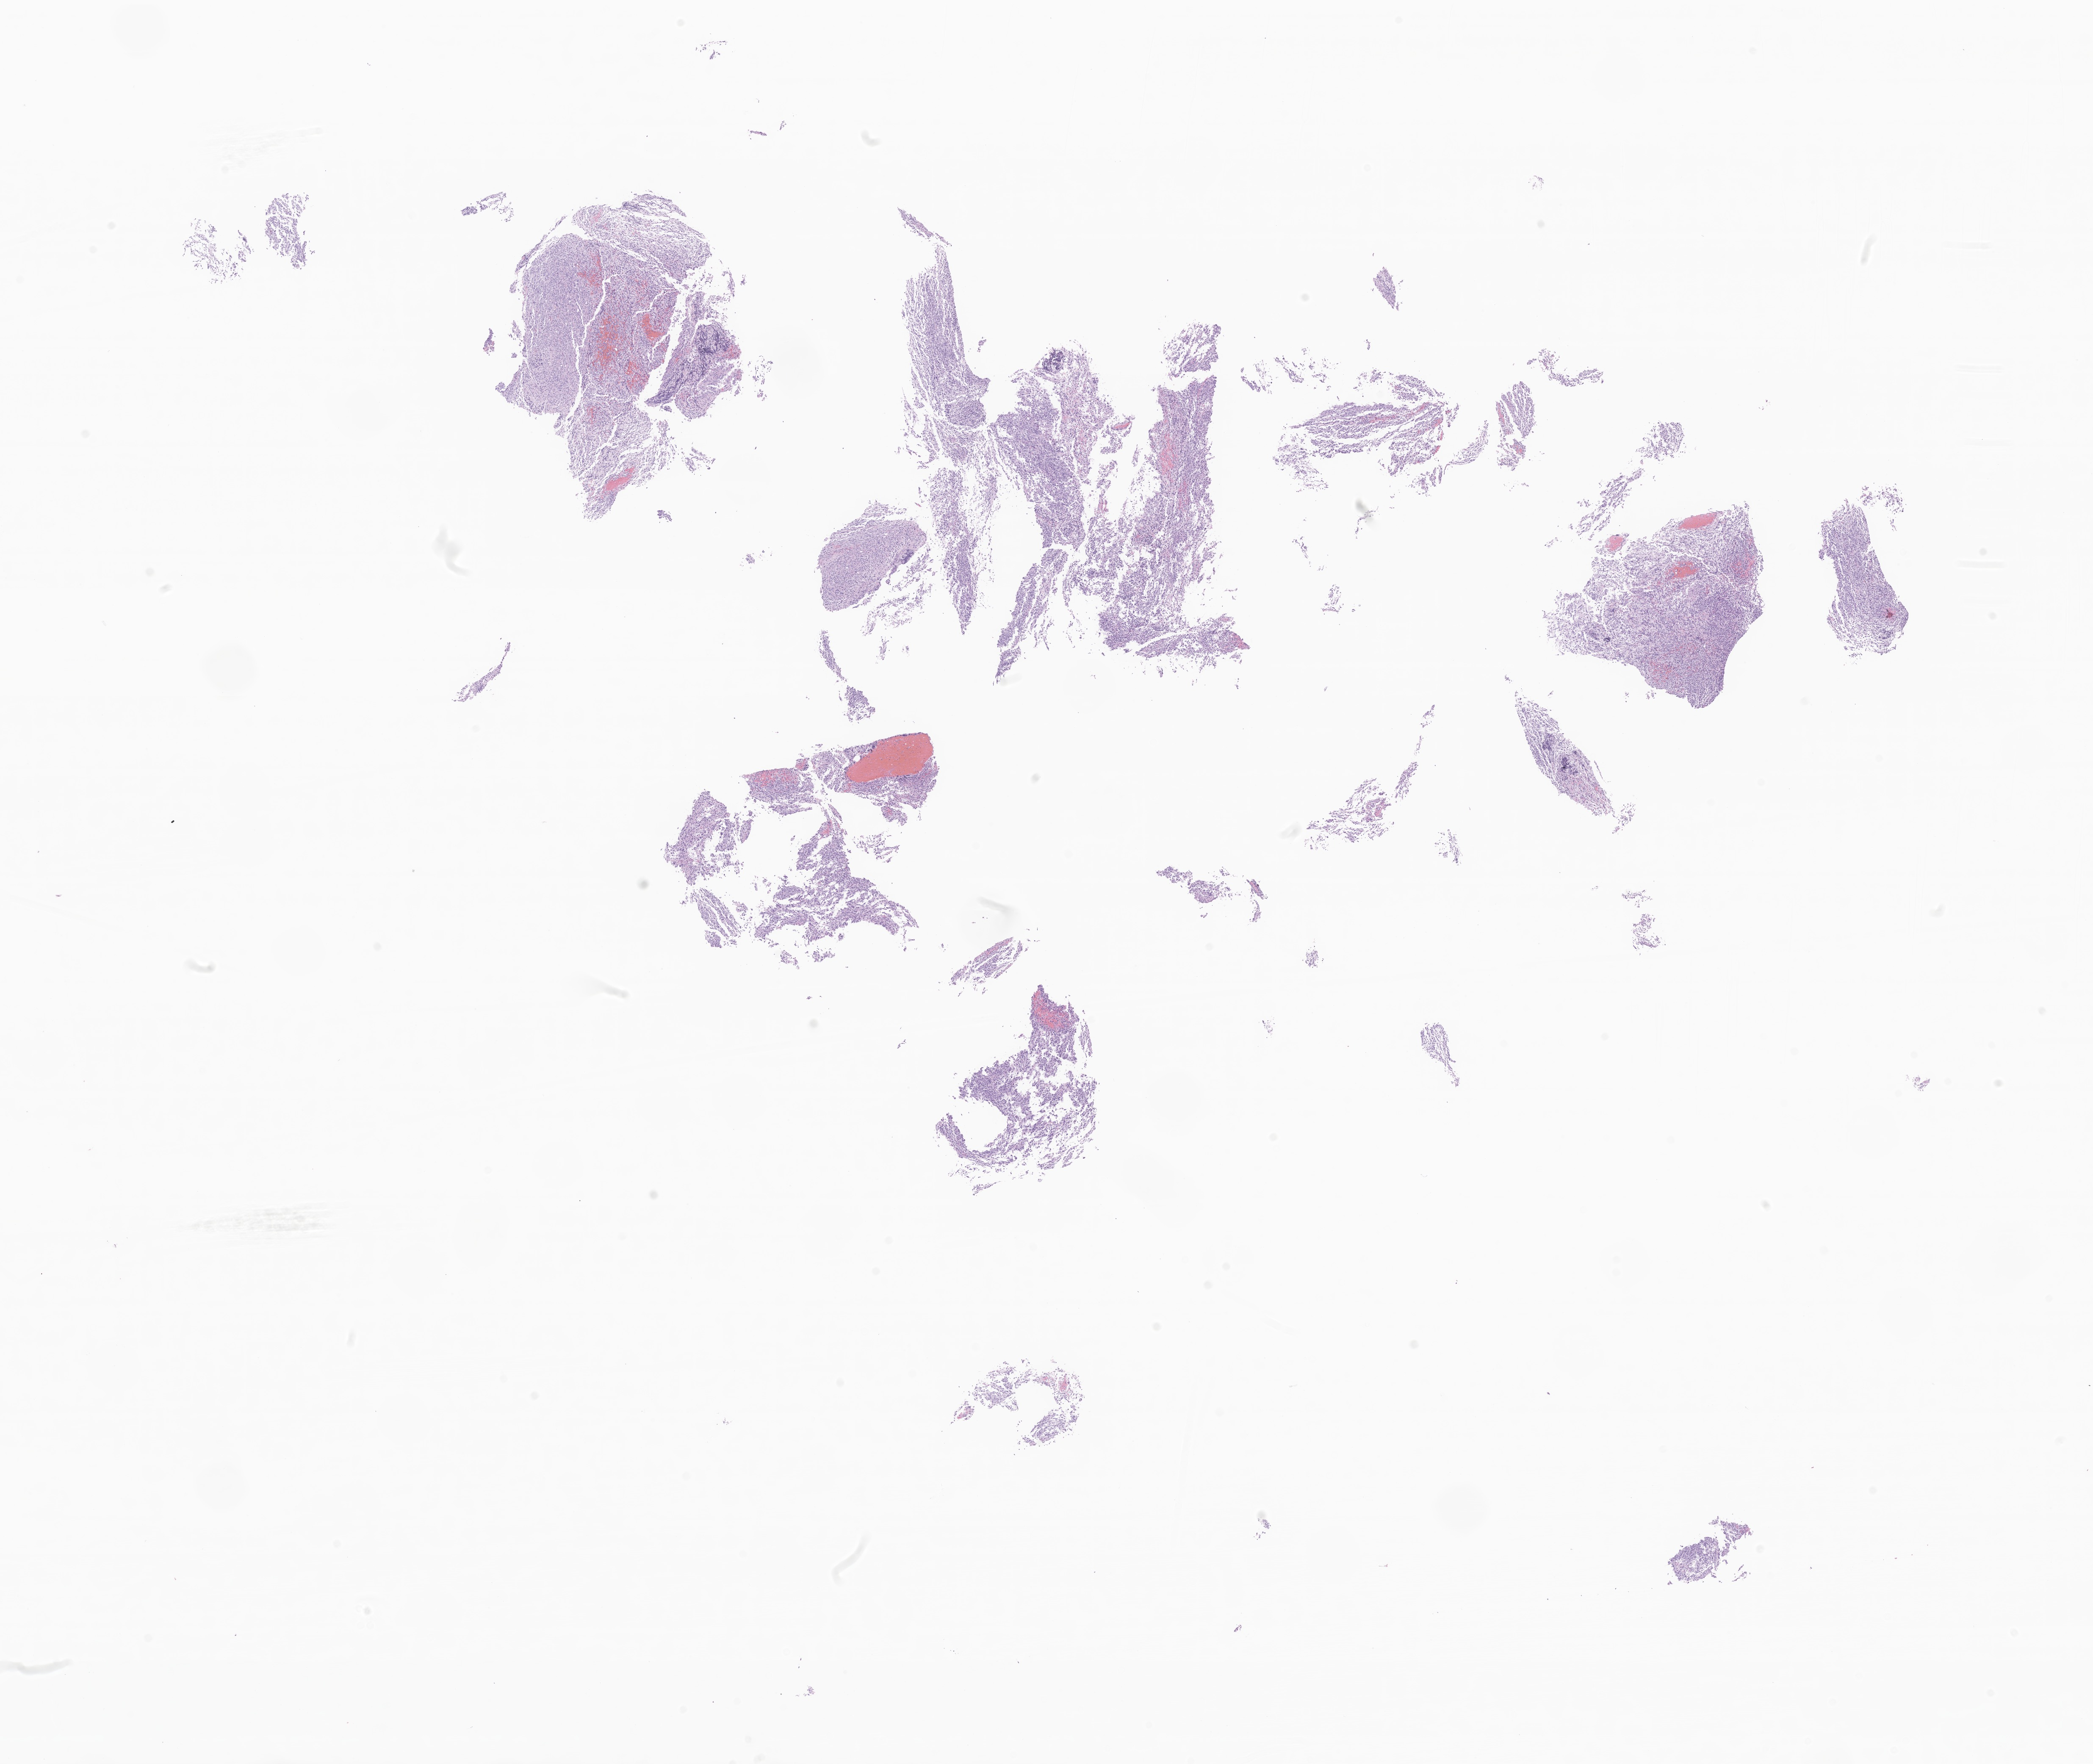
Digitized hematoxylin and eosin (H&E)-stained section of tumor tissue from the brain stem, low-resolution overview of the scanned area, about 20.8 x 17.6 mm, formalin-fixed paraffin-embedded section. Patient: female, age 234 months (19 years 6 months).
Diagnosis (ICD-O-3 morphology term): Neoplasm, malignant.